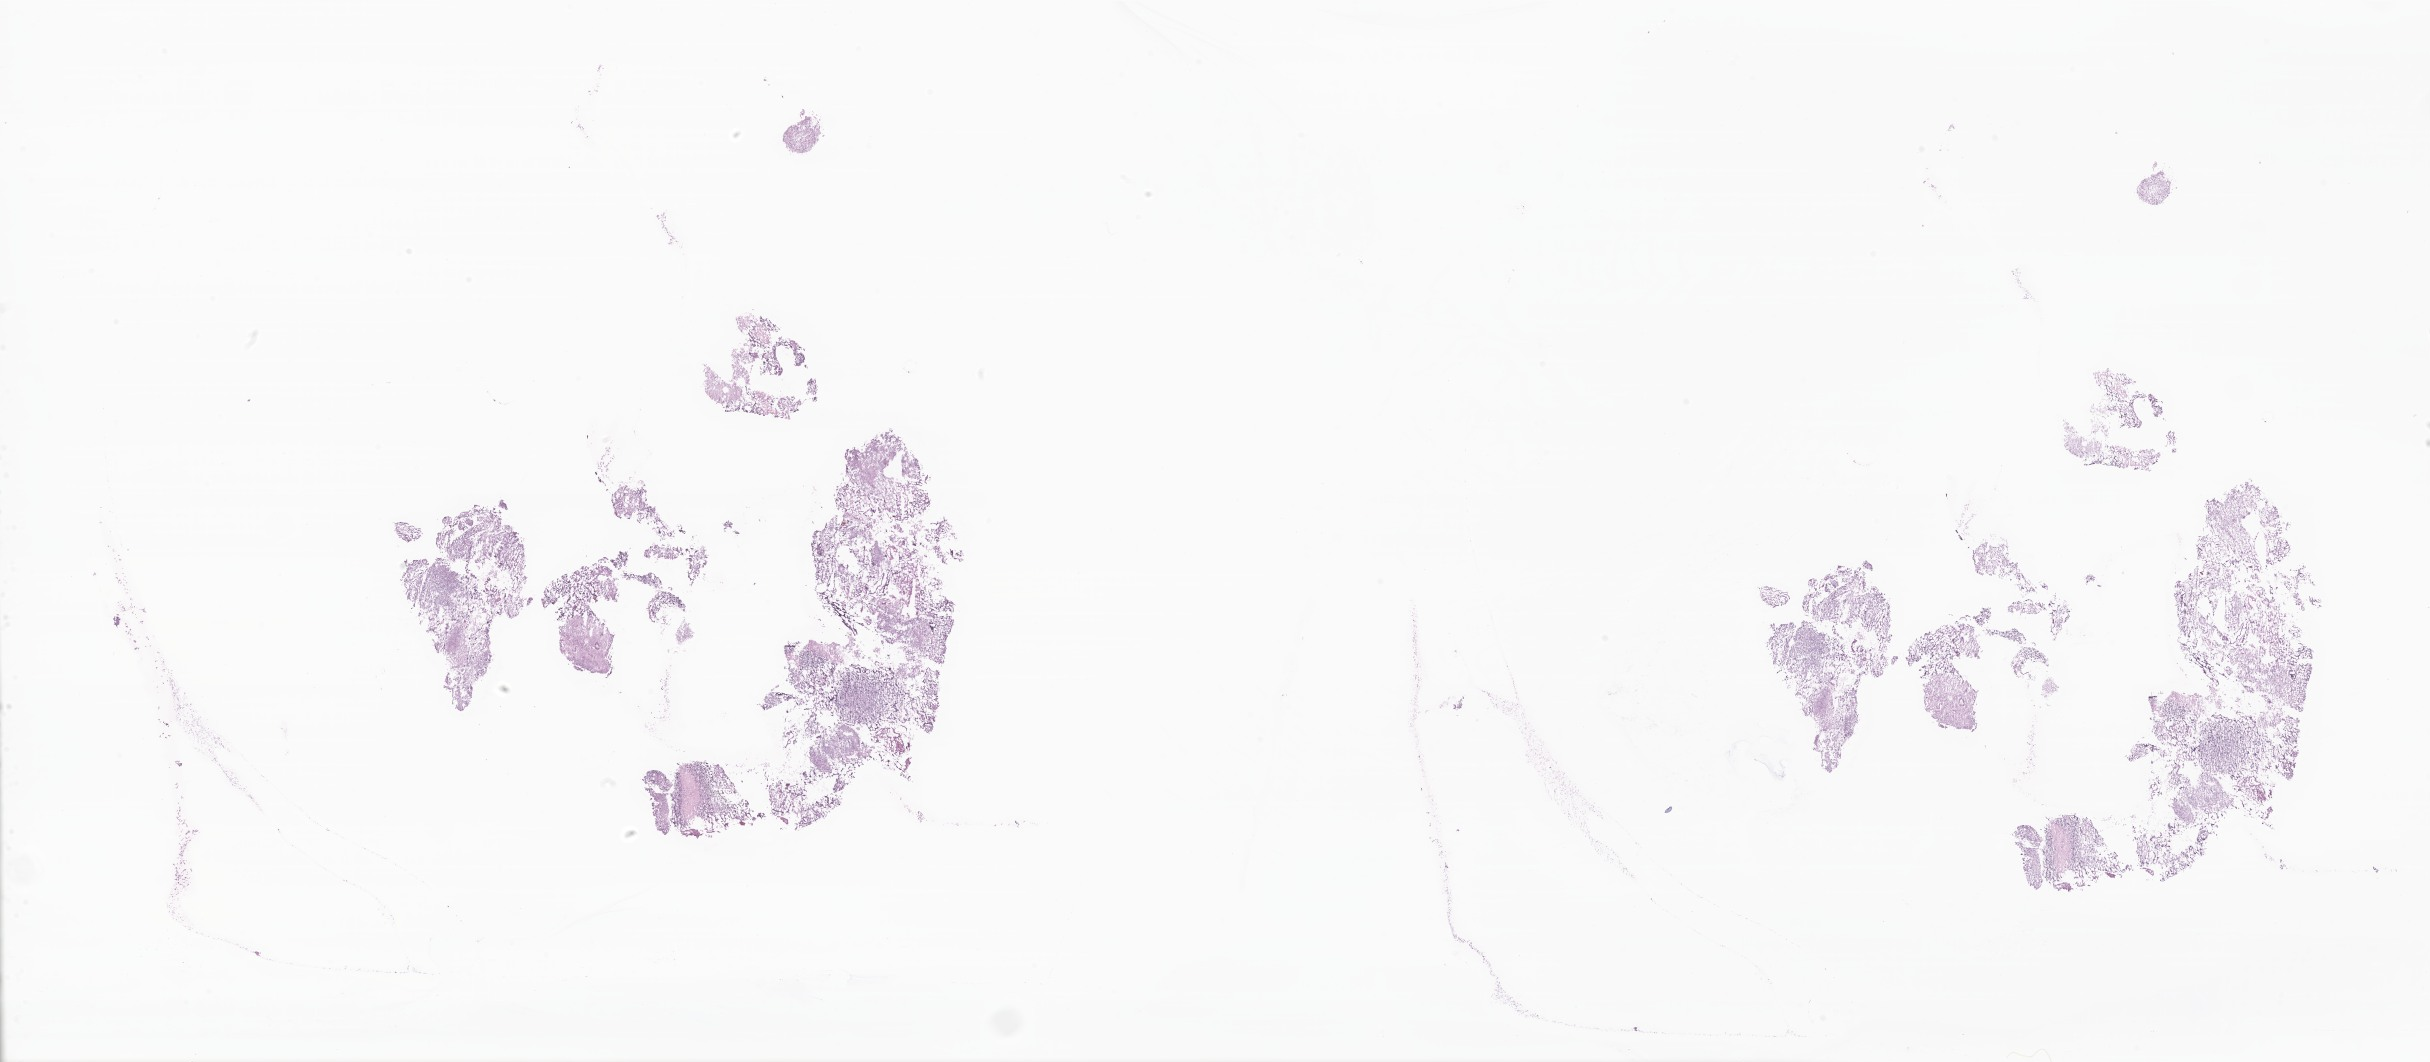
Whole-slide image, H&E stain of tumor tissue from the brain — low-resolution overview of the scanned area, about 41.0 x 17.9 mm. Frozen section. Patient male; age 523 days (about 1.4 years).
Diagnosis (ICD-O-3 morphology term): Ependymoma, NOS.